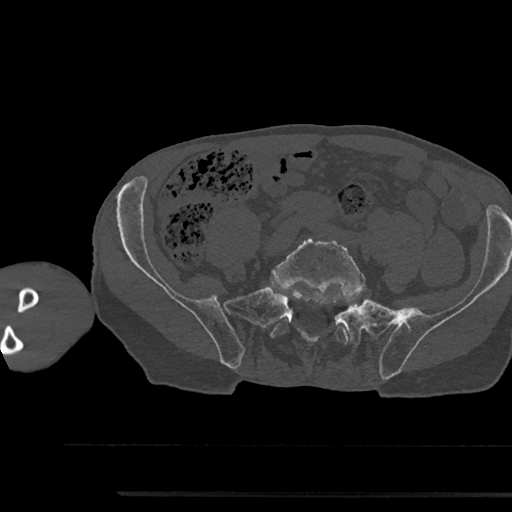
CT including the spine, one axial slice. Slice 318 of 797 in the series (ordered by position). Reconstruction kernel Br40s/3. 120 kVp. Bone window (W 1800 / L 400 HU). 512 × 512 image matrix, field of view 367 × 367 mm. Patient: male, 79 years. From the clinical record (not read from this slice): primary cancer: prostate.
Annotated regions visible in this slice (semi-automatic segmentation, software-assisted and operator-edited):
- L5 vertebra: bounding box [x1, y1, x2, y2] px = [270, 235, 365, 344]